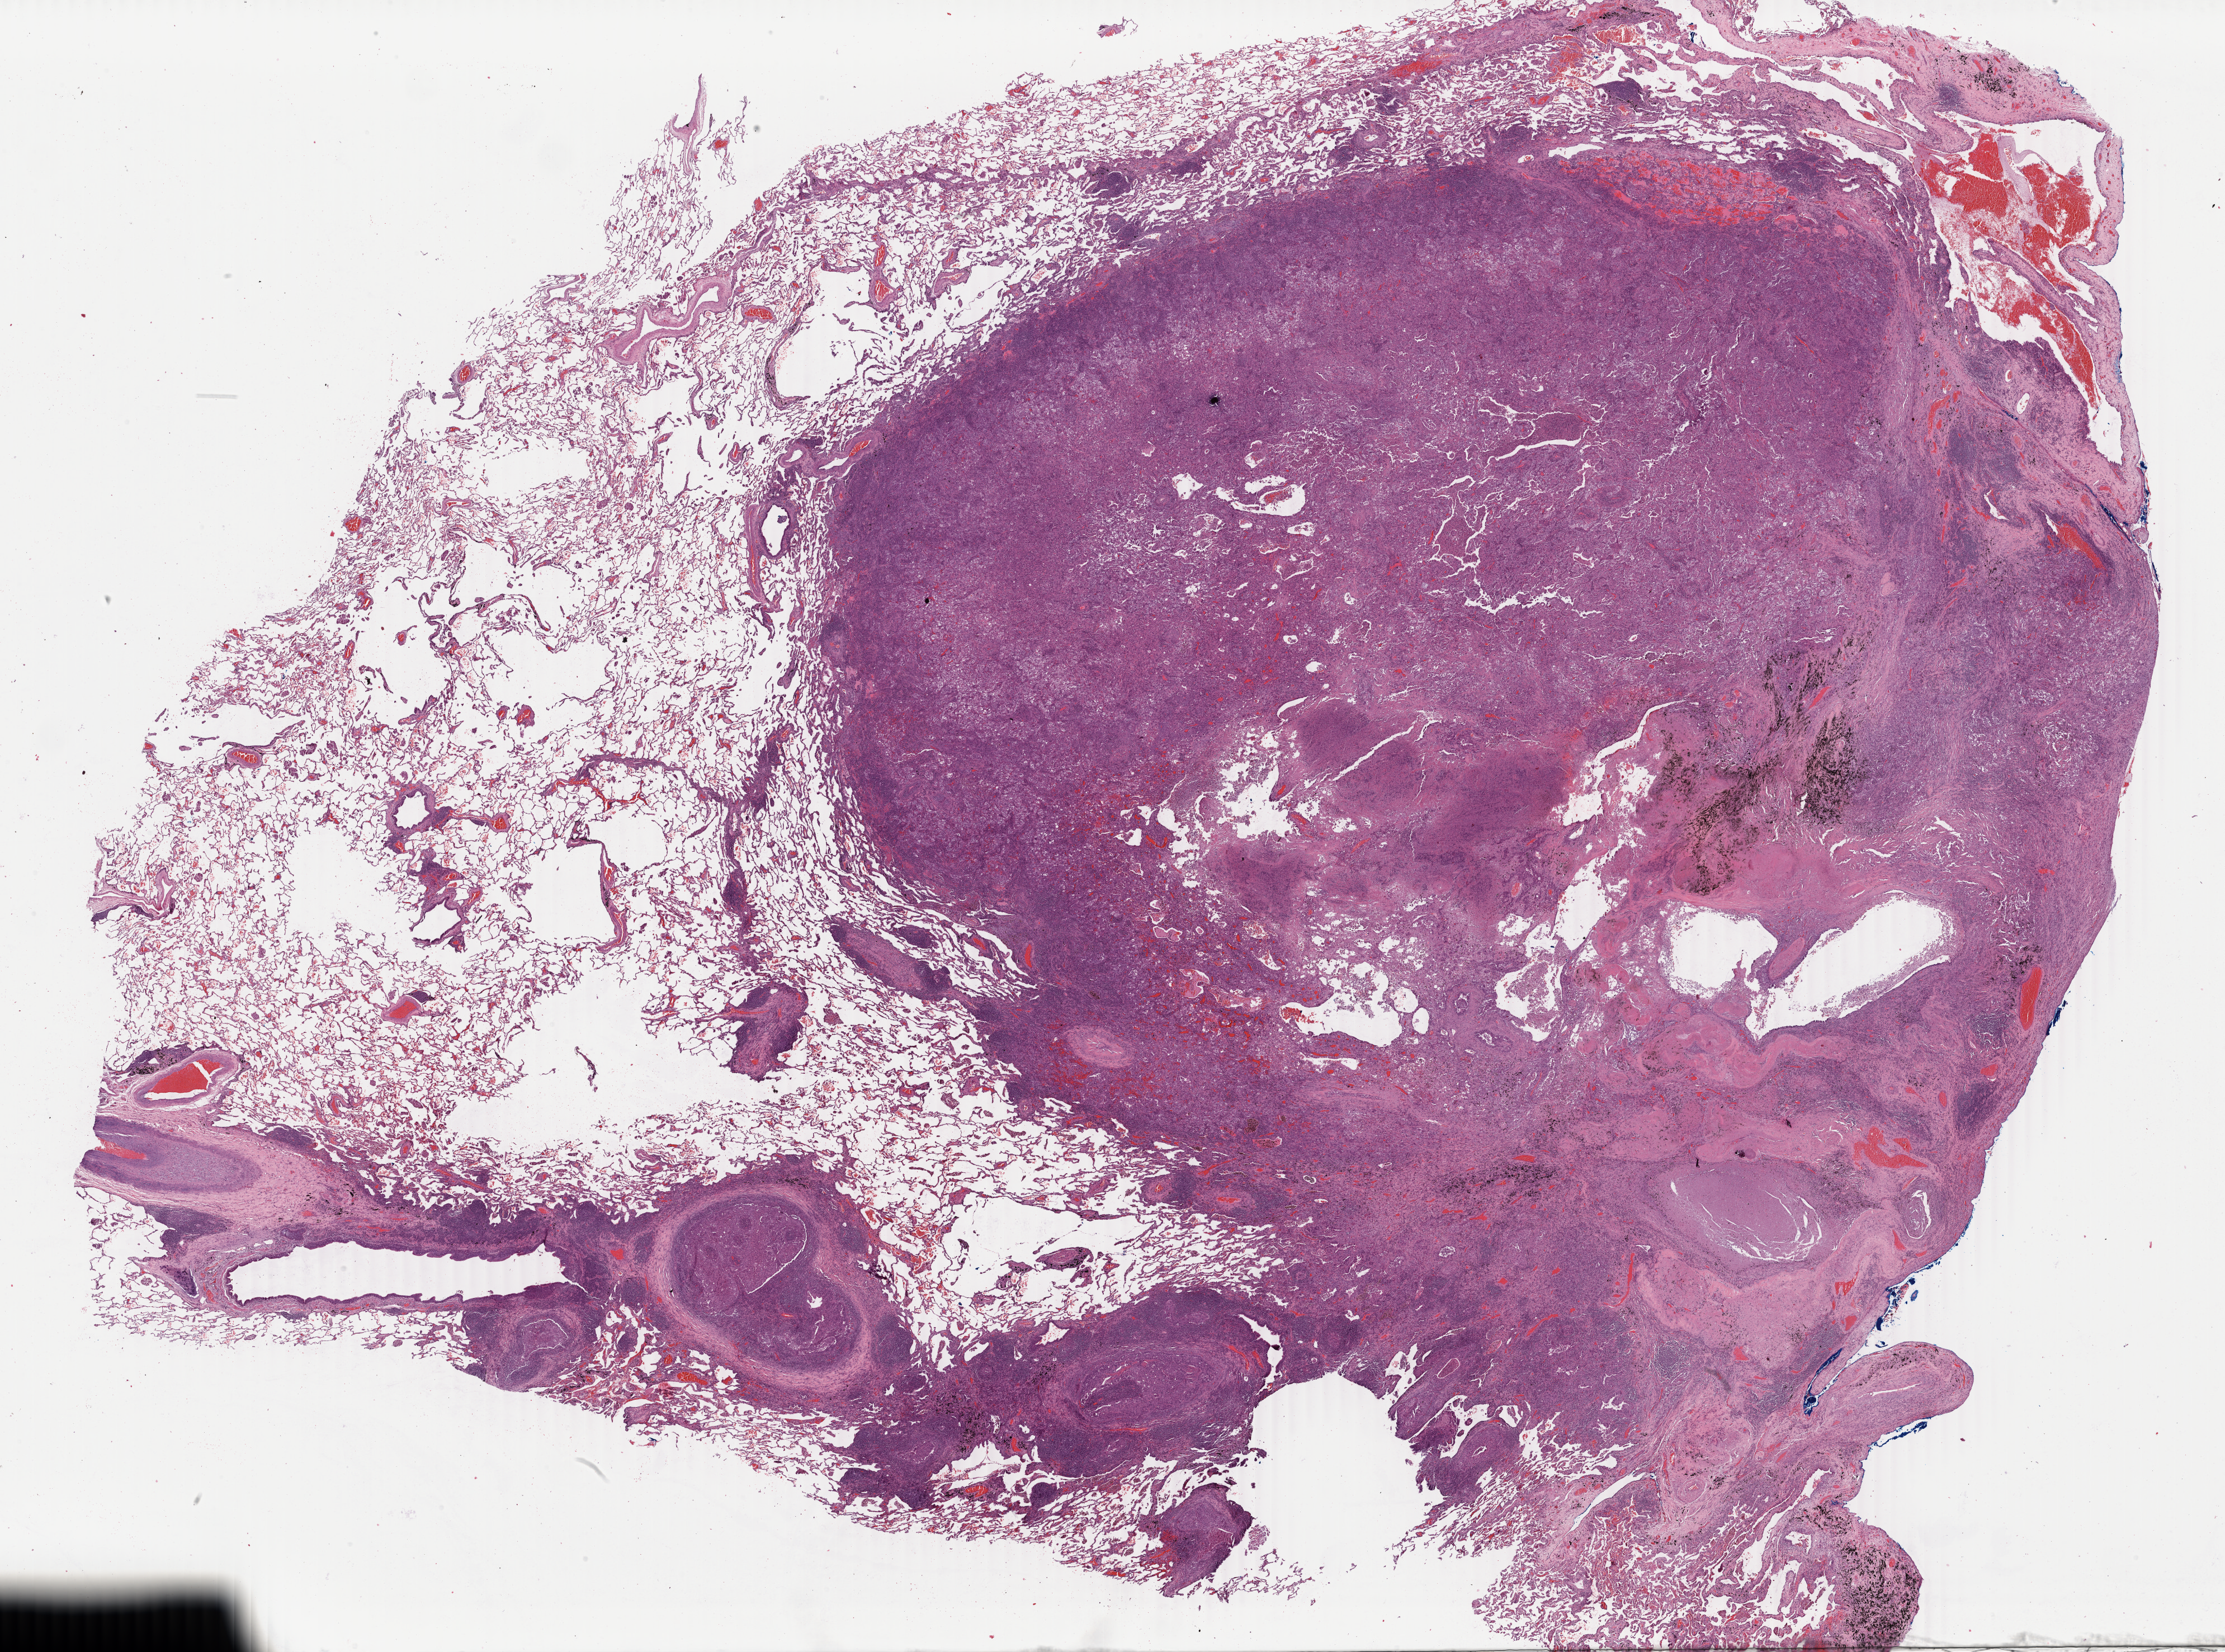
Haematoxylin and eosin whole-slide image, low-resolution overview of the scanned area, about 31.6 x 23.5 mm, specimen: tumor tissue, anatomic site: lung. Patient: male, 59 years old.
Histologic diagnosis: Adenosquamous carcinoma.